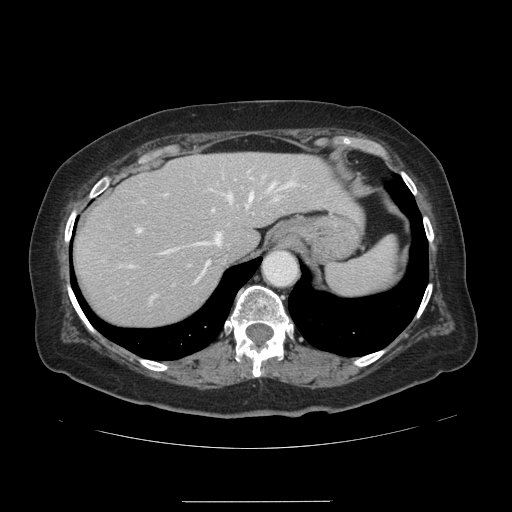
Contrast-enhanced abdominal CT, one axial slice. Position 105 of 141 along the scan axis. Intravenous contrast given. Soft-tissue window (W 400 / L 40 HU). 512 × 512 image matrix, field of view 393 × 393 mm. Female patient, age 74 years. Case-level facts recorded for this patient, not image findings: diagnosis: colorectal cancer liver metastases, imaged before liver resection; multiple liver metastases: yes; largest metastasis: 7 cm; chemotherapy before resection: no.
Structures marked on this image (outlined manually by an expert reader):
- hepatic veins: box from (x=160, y=183) to (x=291, y=283) px
- liver: (x=74, y=153)–(x=358, y=327)
- planned liver remnant (the part of the liver to remain after resection): (x=75, y=153)–(x=358, y=327)
- portal vein (with intrahepatic branches): (x=129, y=194)–(x=247, y=301)